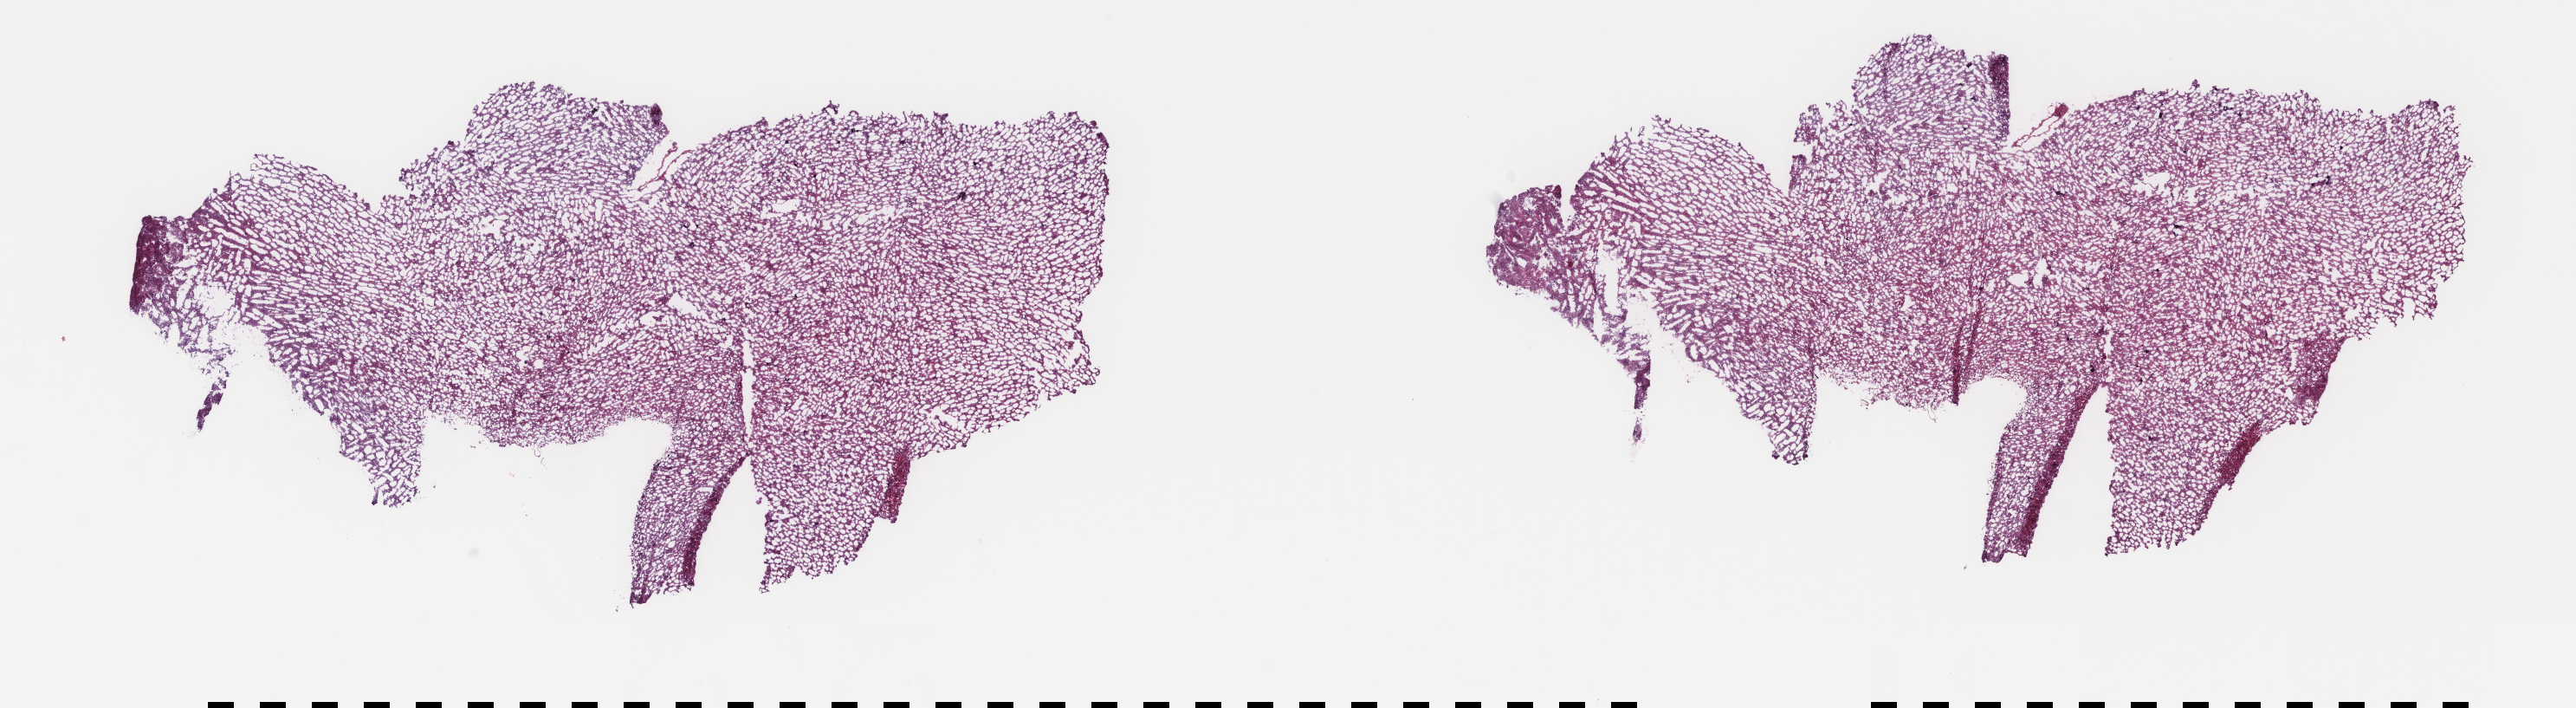
Hematoxylin and eosin (H&E) stained whole-slide image — shown as a low-resolution overview of the whole scanned area (about 23.6 x 6.5 mm), frozen section from the top of the tissue portion, brain, primary tumour sample. Female, age 53 years at initial diagnosis.
Diagnosis: Oligodendroglioma, NOS.